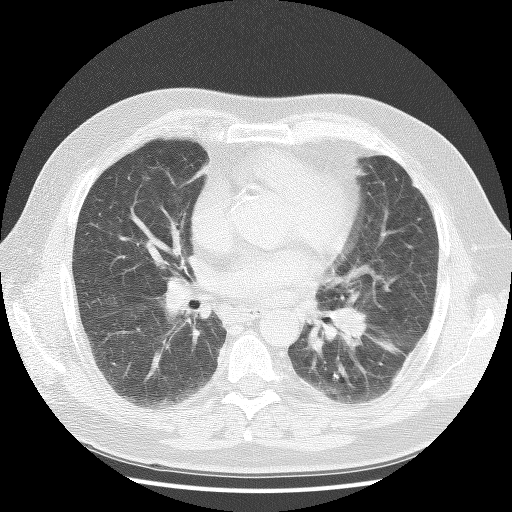
Chest CT (low-dose screening protocol), one axial image, first (baseline) screen, lung window (W 1500 / L -600 HU), lung (sharp) reconstruction kernel (BONE), slice 51 of 111 in the series. Male participant, aged 59 years at enrolment. Current smoker at enrolment.
Lesion marked by an expert reader, bounding box <305,287,379,359> (left, top, right, bottom; pixels). Screening reader's record for this exam (one nodule recorded; not confirmed to be the boxed lesion): non-calcified nodule or mass ≥4 mm, right upper lobe, 4 × 4 mm, soft tissue attenuation. Note: the box lies in the patient's left hemithorax on this image, whereas the reader's record names the right lung; they may be different findings. Official screen result: positive, change unspecified: nodule(s) >= 4 mm or enlarging nodule(s), mass(es), or other non-specific abnormalities suspicious for lung cancer. Later outcome: lung cancer diagnosed 20 days after this screen — non-small cell carcinoma, left hilum, stage IV (AJCC 6th edition).